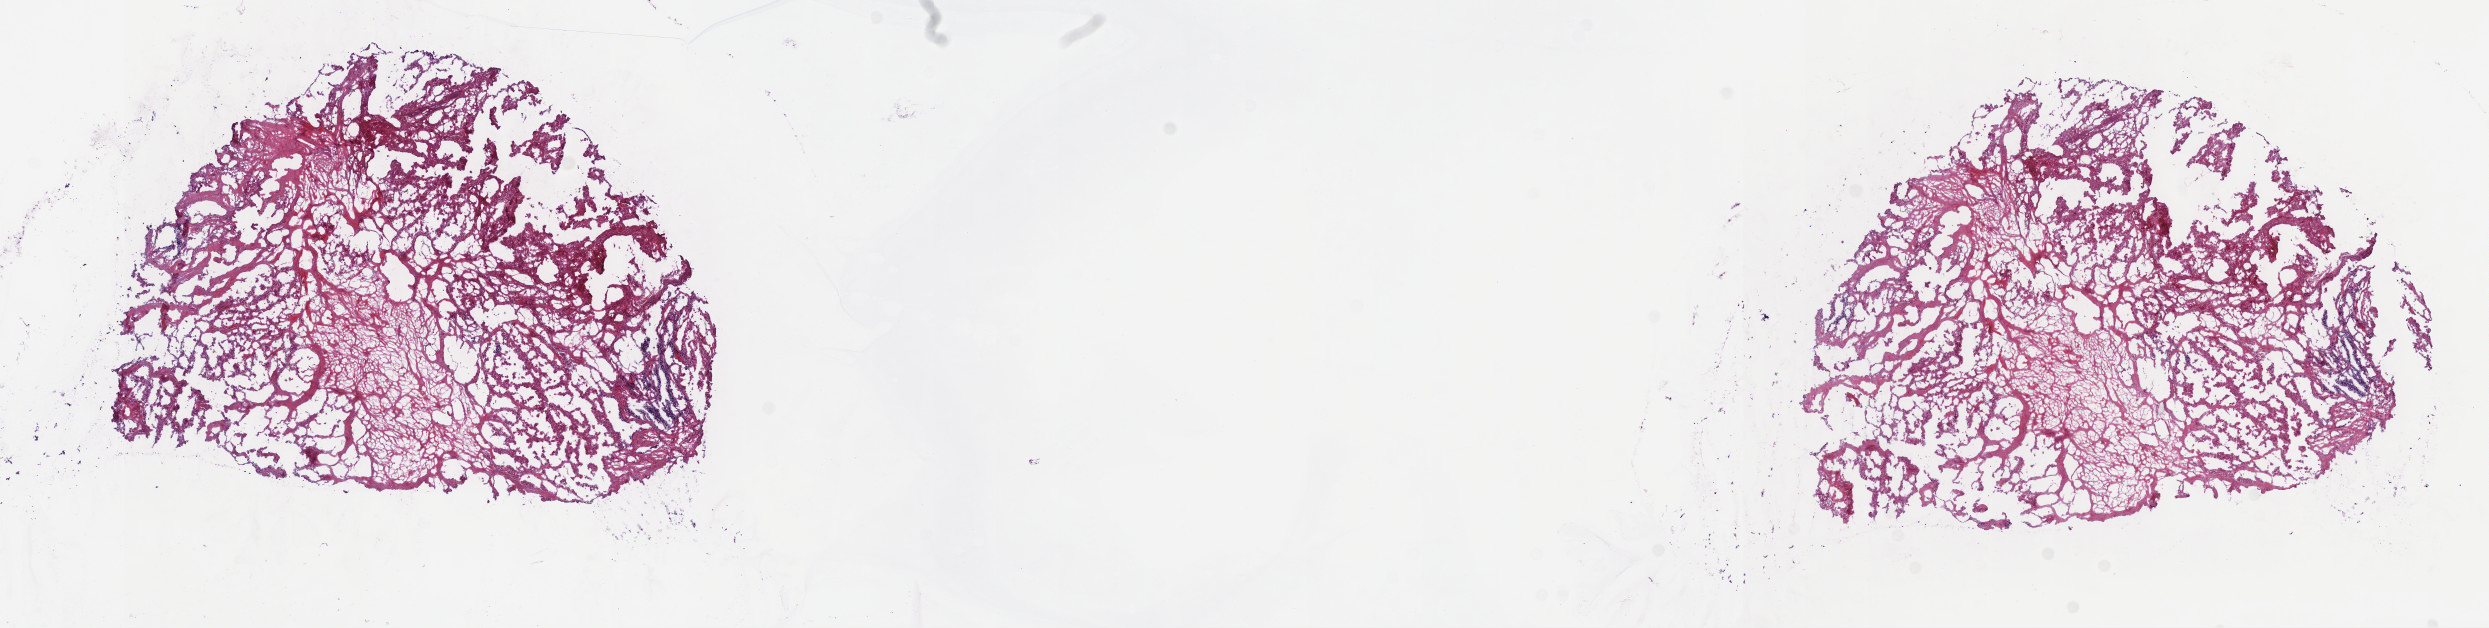
Whole-slide histology image, H&E-stained — whole scanned area (about 20.1 x 5.1 mm, from a 40x scan) shown as a low-resolution overview; formalin-fixed paraffin-embedded (FFPE) diagnostic section; sample: primary tumour, breast. Female, age 29 years at initial diagnosis.
• pathologic diagnosis: Infiltrating duct carcinoma, NOS
• AJCC pathologic stage: IIIB (7th edition)
• TNM: T4b N2 M0